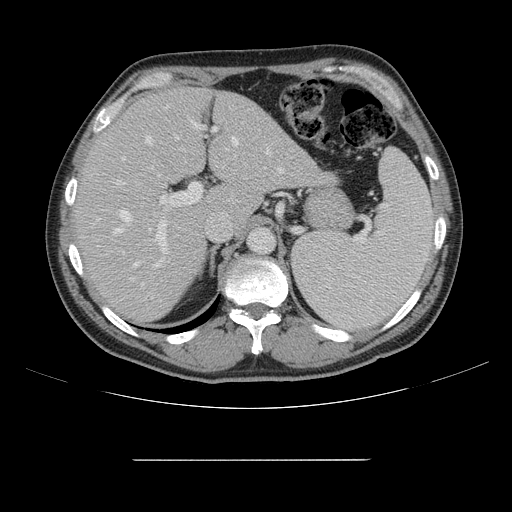
Contrast-enhanced abdominal CT, one axial slice. Position 103 of 164 along the scan axis. Intravenous contrast given. Soft-tissue window (W 400 / L 40 HU). 512 × 512 image matrix, field of view 404 × 404 mm. Male patient, age 54 years. Case-level facts recorded for this patient, not image findings: diagnosis: colorectal cancer liver metastases, imaged before liver resection; multiple liver metastases: yes.
Annotated regions visible in this slice (manually delineated by an expert):
- hepatic veins: bounding box <114,137,284,268> (left, top, right, bottom; pixels)
- liver: <73,87,329,324>
- planned liver remnant (the part of the liver to remain after resection): <73,87,238,323>
- portal vein (with intrahepatic branches): <118,105,218,301>